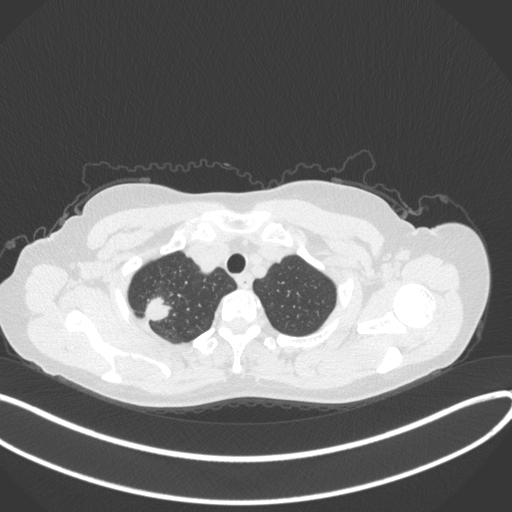
Chest CT, one axial slice; position 320 of 342 along the scan axis; reconstruction kernel B31f; lung window (W 1500 / L -600 HU); 1 mm slice thickness; 512 × 512 image matrix, field of view 400 × 400 mm. Patient: female, 50 years. Case-level facts recorded for this patient, not image findings: clinical TNM (as recorded): T1c N0 M0; histopathological grade: G2-3.
Annotated regions visible in this slice (bounding box drawn by a radiologist):
- lung tumour (recorded histology: adenocarcinoma): box from (x=139, y=293) to (x=172, y=321) px